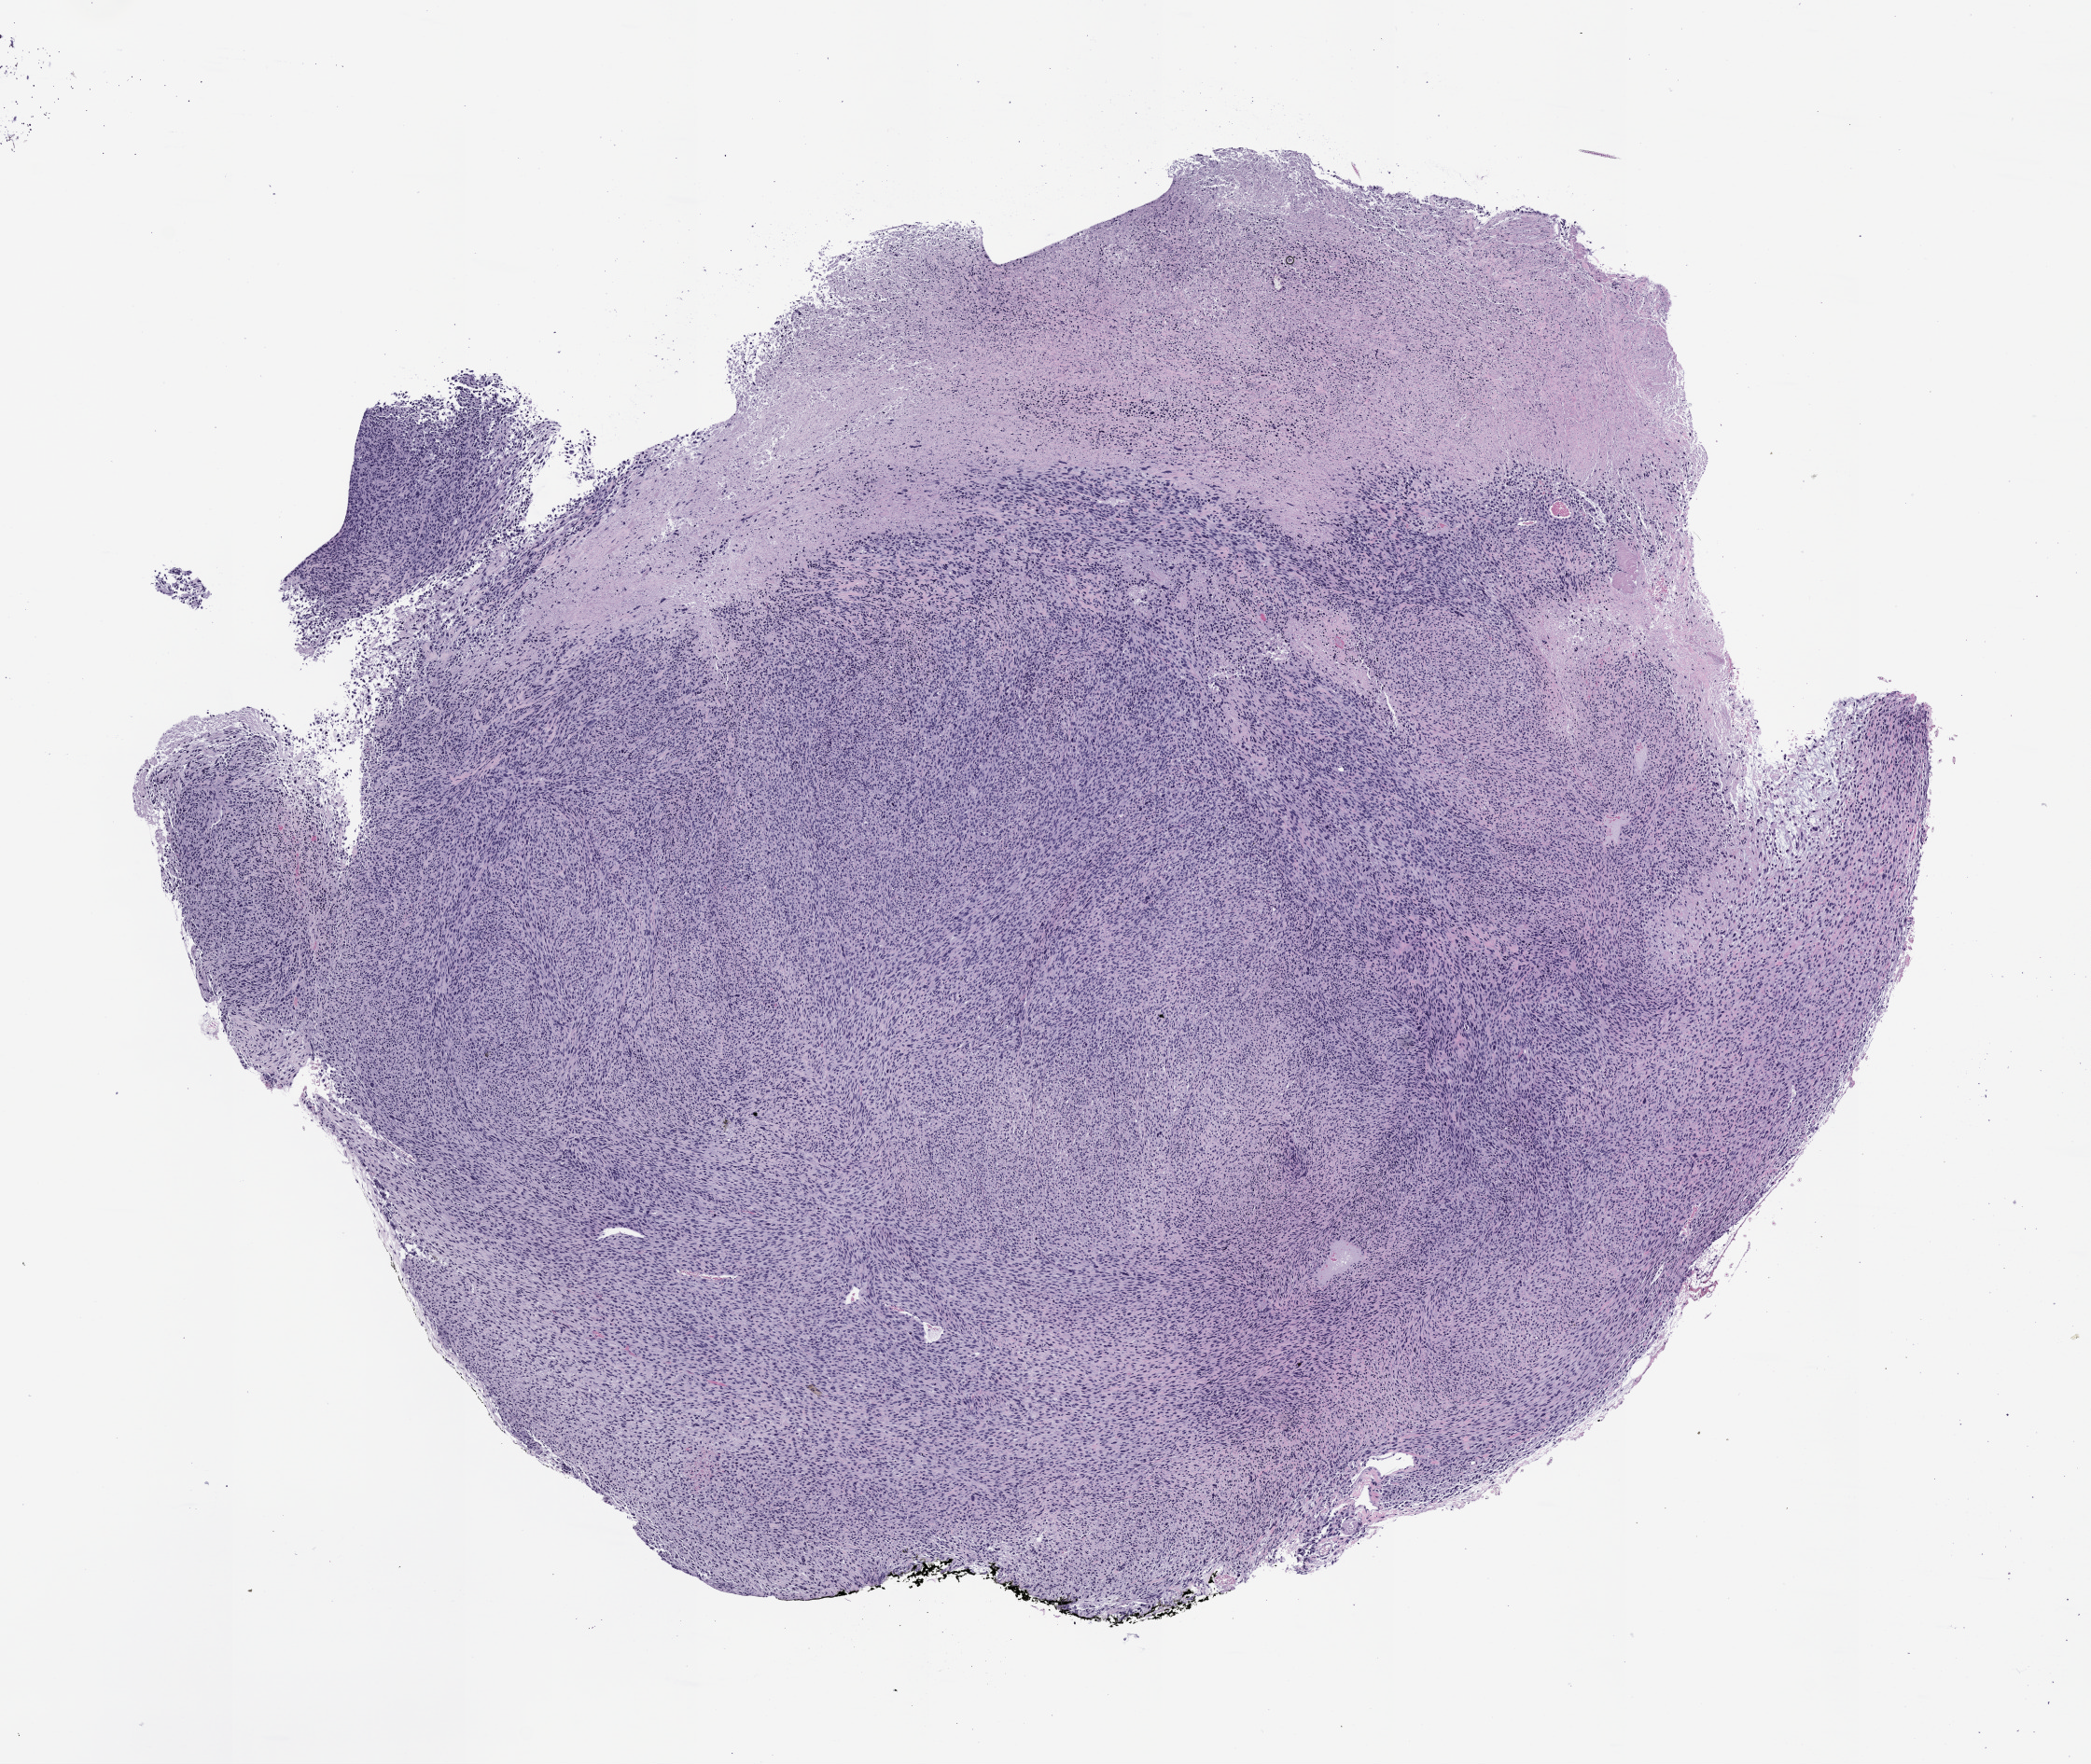
Hematoxylin and eosin (H&E) whole-slide image of a patient-derived xenograft (PDX) tumor grown in a mouse, passage 1 — shown as a low-resolution overview of the whole scanned area (about 9.0 x 7.6 mm); formalin-fixed paraffin-embedded section; originating tumor site category: musculoskeletal.
• originating patient diagnosis: Non-Rhabdo. soft tissue sarcoma